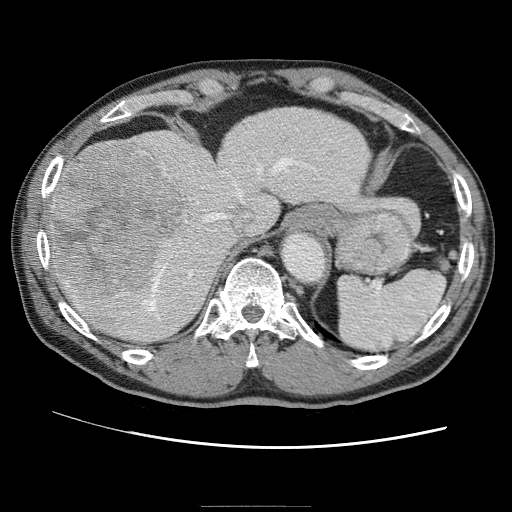
Contrast-enhanced abdominal CT (liver protocol), one axial slice. Position 47 of 75 along the scan axis. Reconstruction kernel STANDARD. 120 kVp. One of 2 acquisitions stored at this slice position. Soft-tissue window (W 400 / L 40 HU). 2.5 mm slice thickness. 512 × 512 image matrix, field of view 360 × 360 mm. From the clinical record (not read from this slice): diagnosis: hepatocellular carcinoma (patient treated with transarterial chemoembolisation; whether this scan precedes or follows treatment is not stated here); TNM stage (as recorded): Stage-II; Child-Pugh class: A; tumour nodularity: multinodular.
Outlined on this slice (semi-automatic segmentation, software-assisted and operator-edited):
- abdominal aorta: bounding box <281,233,324,282> (left, top, right, bottom; pixels)
- liver parenchyma outside the tumour (the mass and vessels are separate outlines, so this box may not span the whole liver): <48,107,374,344>
- mass: <49,144,188,299>
- liver vessels: <147,158,251,303>